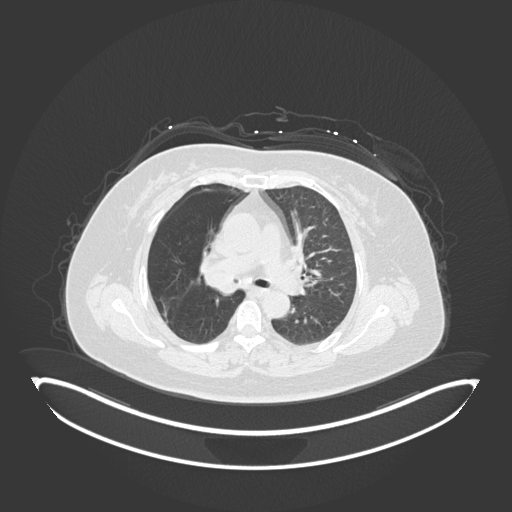
Chest CT, one axial slice. 120 kVp. Lung window (W 1500 / L -600 HU). 1 mm slice thickness. 512 × 512 image matrix, field of view 500 × 500 mm. Patient: female, 60 years. Case-level facts recorded for this patient, not image findings: clinical TNM (as recorded): T1c N0 M0; histopathological grade: G1-G2.
Annotated regions visible in this slice (rectangle marked by the reading radiologist):
- lung tumour (recorded histology: squamous cell carcinoma): bounding box <201,256,244,298> (left, top, right, bottom; pixels)